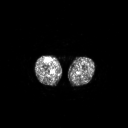
FDG PET of an extremity soft-tissue mass (from a PET/CT study), one axial slice. 128 × 128 image matrix, field of view 700 × 700 mm. Male patient, age 56 years. From the clinical record (not read from this slice): histological type: pleiomorphic leiomyosarcoma; grade: intermediate; site of the primary tumour: right thigh.
Outlined on this slice (expert contour drawn on MRI and transferred to this co-registered scan by the dataset authors):
- gross tumour volume including surrounding oedema: bounding box [x1, y1, x2, y2] px = [45, 58, 51, 62]